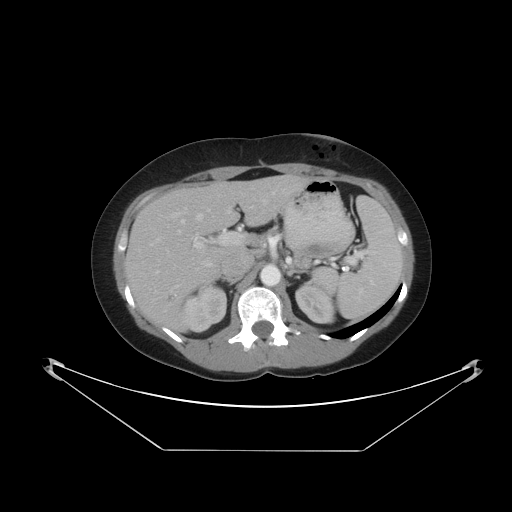
Contrast-enhanced abdominal CT, one axial slice; position 28 of 48 along the scan axis; reconstruction kernel STANDARD; intravenous contrast given; soft-tissue window (W 400 / L 40 HU); 5 mm slice thickness; 512 × 512 image matrix, field of view 482 × 482 mm. Female patient, age 38 years. From the clinical record (not read from this slice): diagnosis: colorectal cancer liver metastases, imaged before liver resection; multiple liver metastases: yes; largest metastasis: 2.5 cm; chemotherapy before resection: no.
Structures marked on this image (expert manual segmentation):
- hepatic veins: bounding box [x1, y1, x2, y2] px = [196, 192, 246, 221]
- liver: [126, 177, 304, 332]
- planned liver remnant (the part of the liver to remain after resection): [162, 177, 304, 249]
- portal vein (with intrahepatic branches): [178, 191, 276, 267]